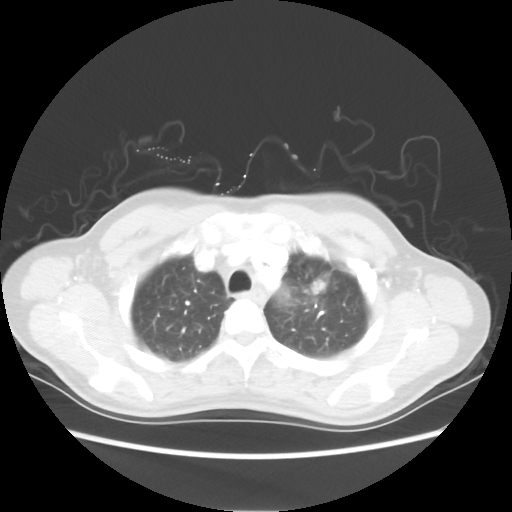
Chest CT, one axial slice; position 44 of 54 along the scan axis; reconstruction kernel STANDARD; 80 kVp; lung window (W 1500 / L -600 HU); 5 mm slice thickness; 512 × 512 image matrix, field of view 360 × 360 mm. Patient: female, 53 years. From the clinical record (not read from this slice): clinical TNM (as recorded): T1c N0 M0.
Structures marked on this image (rectangle marked by the reading radiologist):
- lung tumour (recorded histology: adenocarcinoma): bounding box [x1, y1, x2, y2] px = [304, 277, 328, 301]